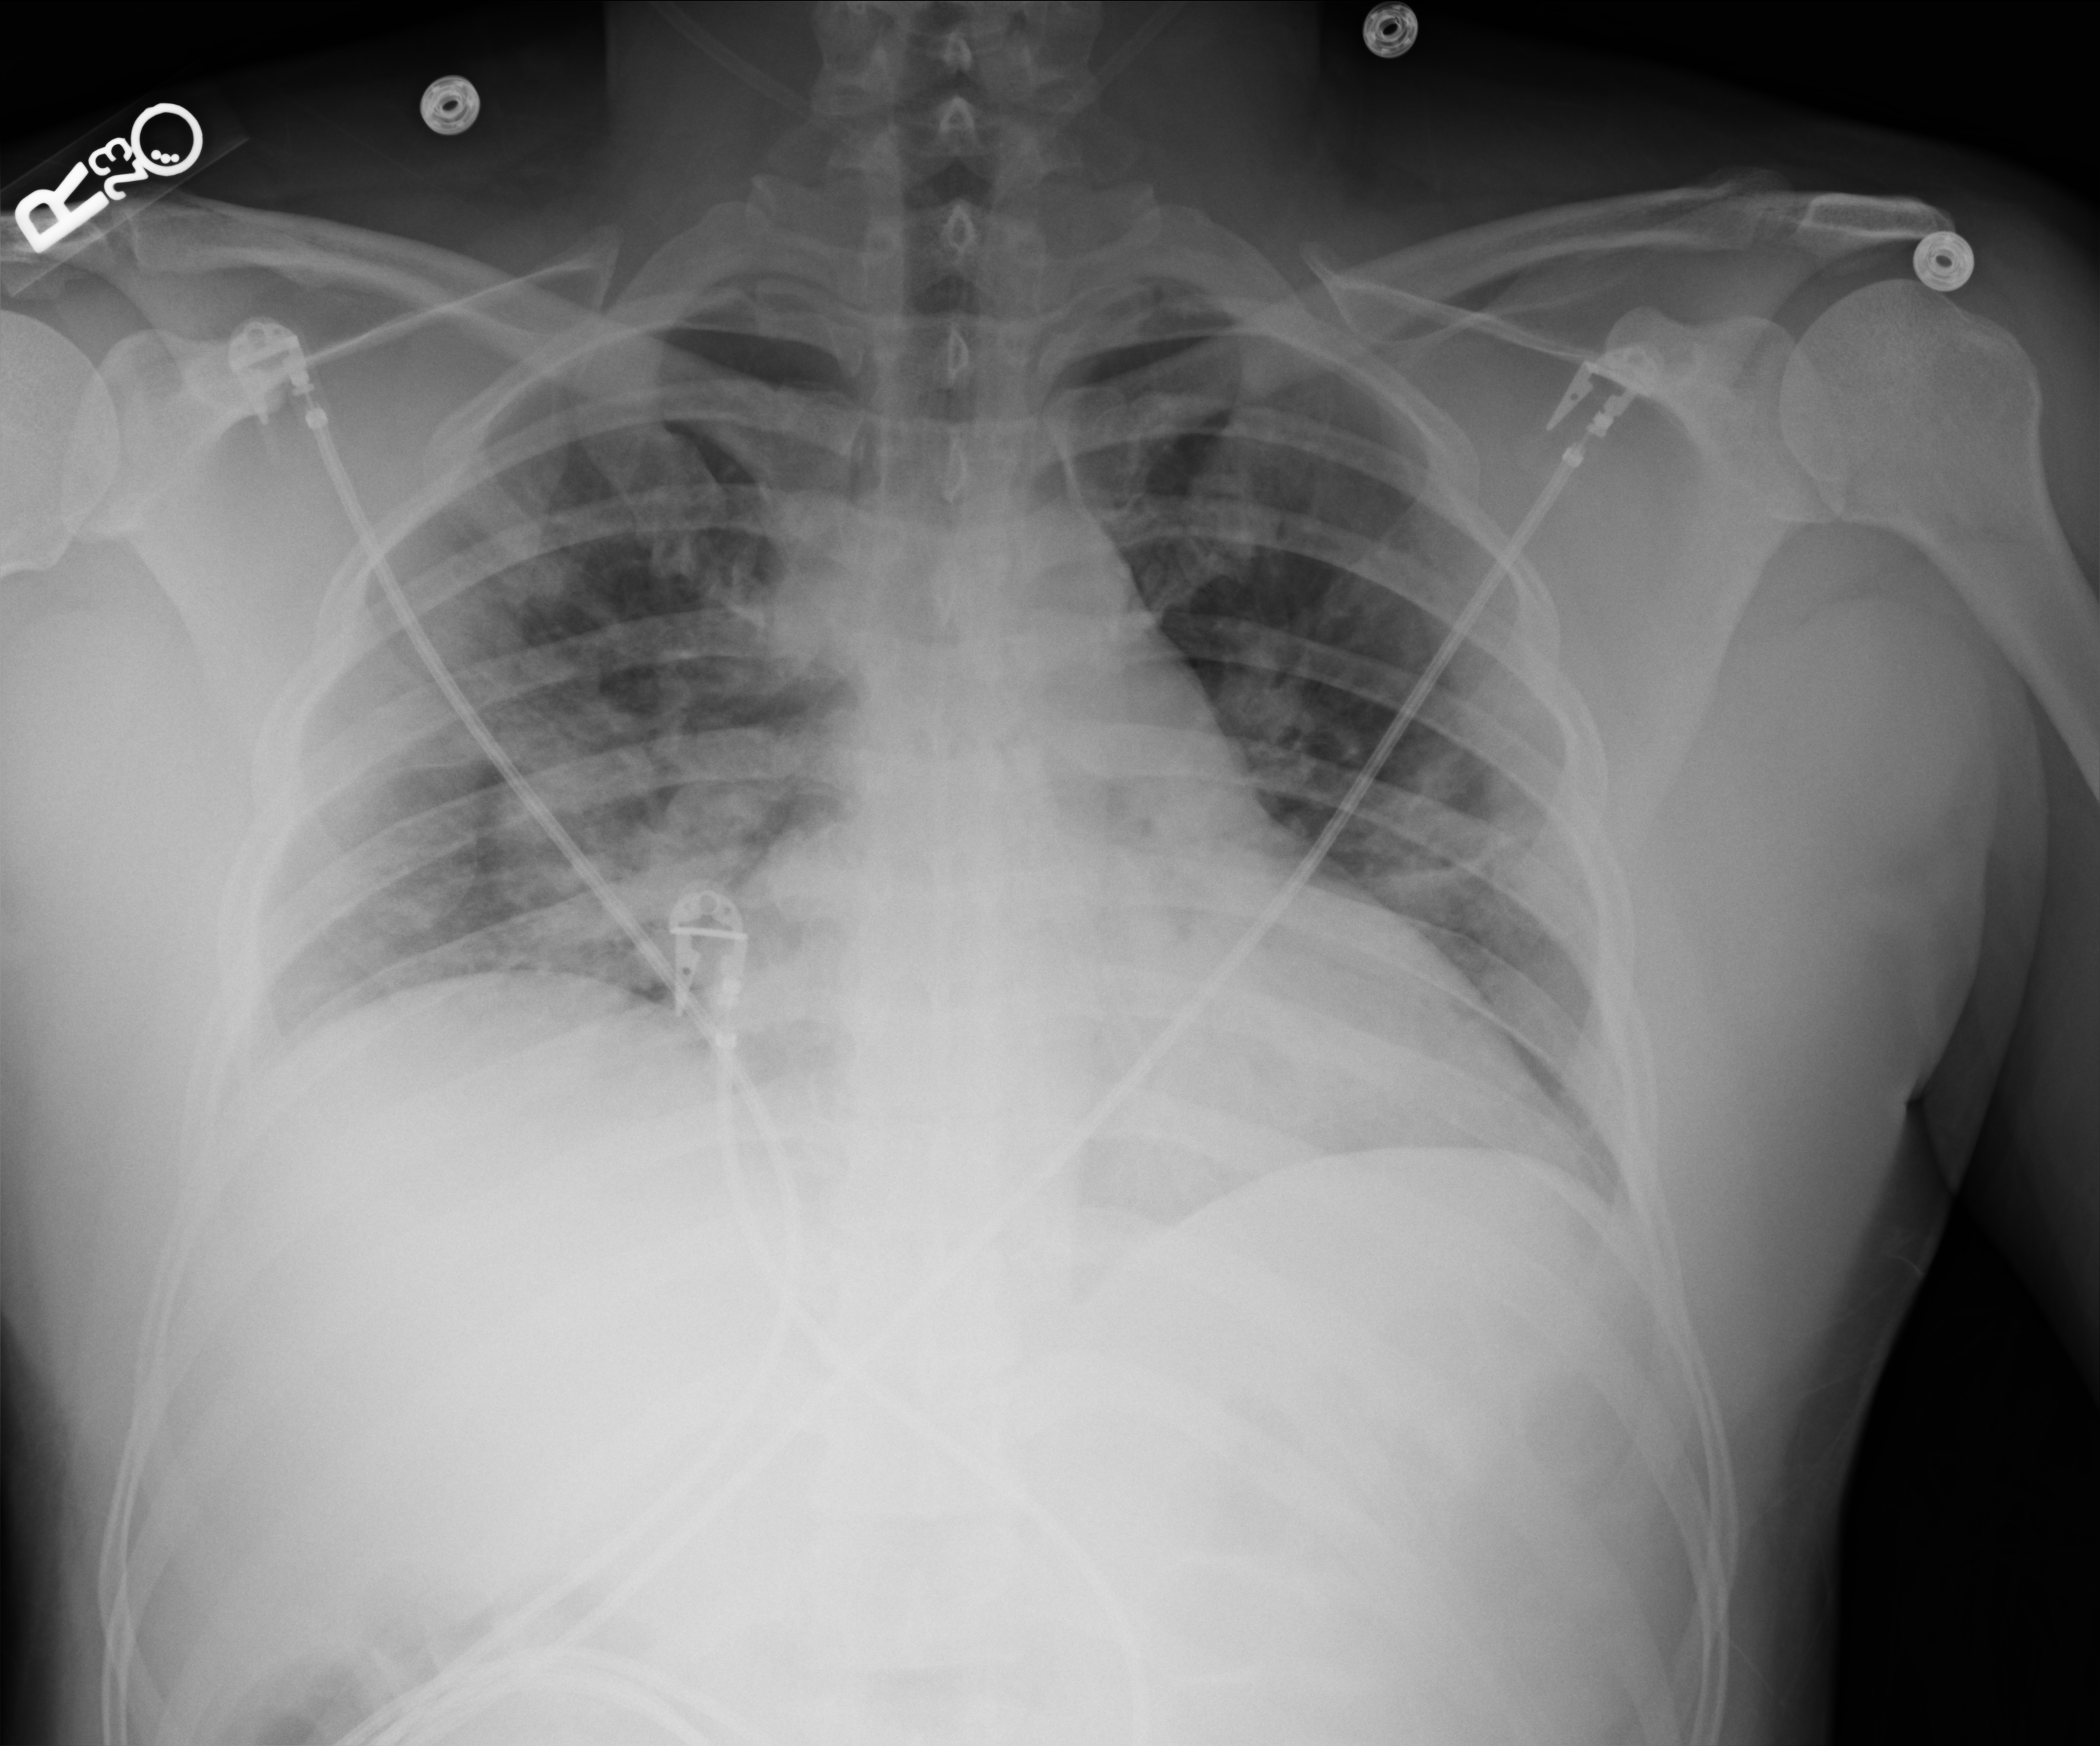
Chest X-ray (portable), anteroposterior (AP) projection. Male patient hospitalised with COVID-19, age 18–59 years.
Hospital-stay facts (about this admission, not read from this image; timing relative to this image not recorded):
- admitted to intensive care during this hospital stay: no